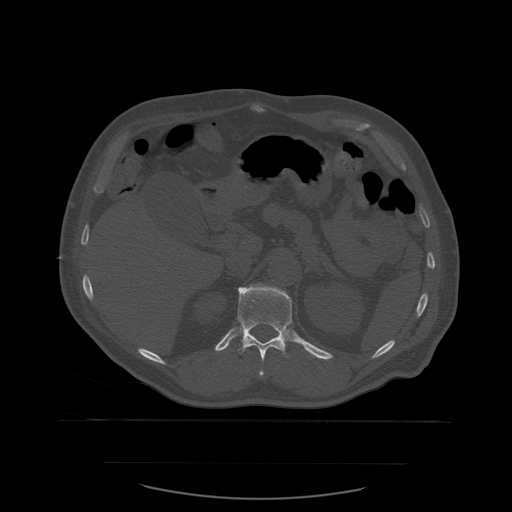
CT including the spine, one axial slice; position 271 of 590 along the scan axis; bone window (W 1800 / L 400 HU); 1.25 mm slice thickness; 512 × 512 image matrix. Patient age 71 years. From the clinical record (not read from this slice): primary cancer: lung.
Outlined on this slice (semi-automatically segmented with operator editing):
- T12 vertebra: bounding box <237,284,293,377> (left, top, right, bottom; pixels)